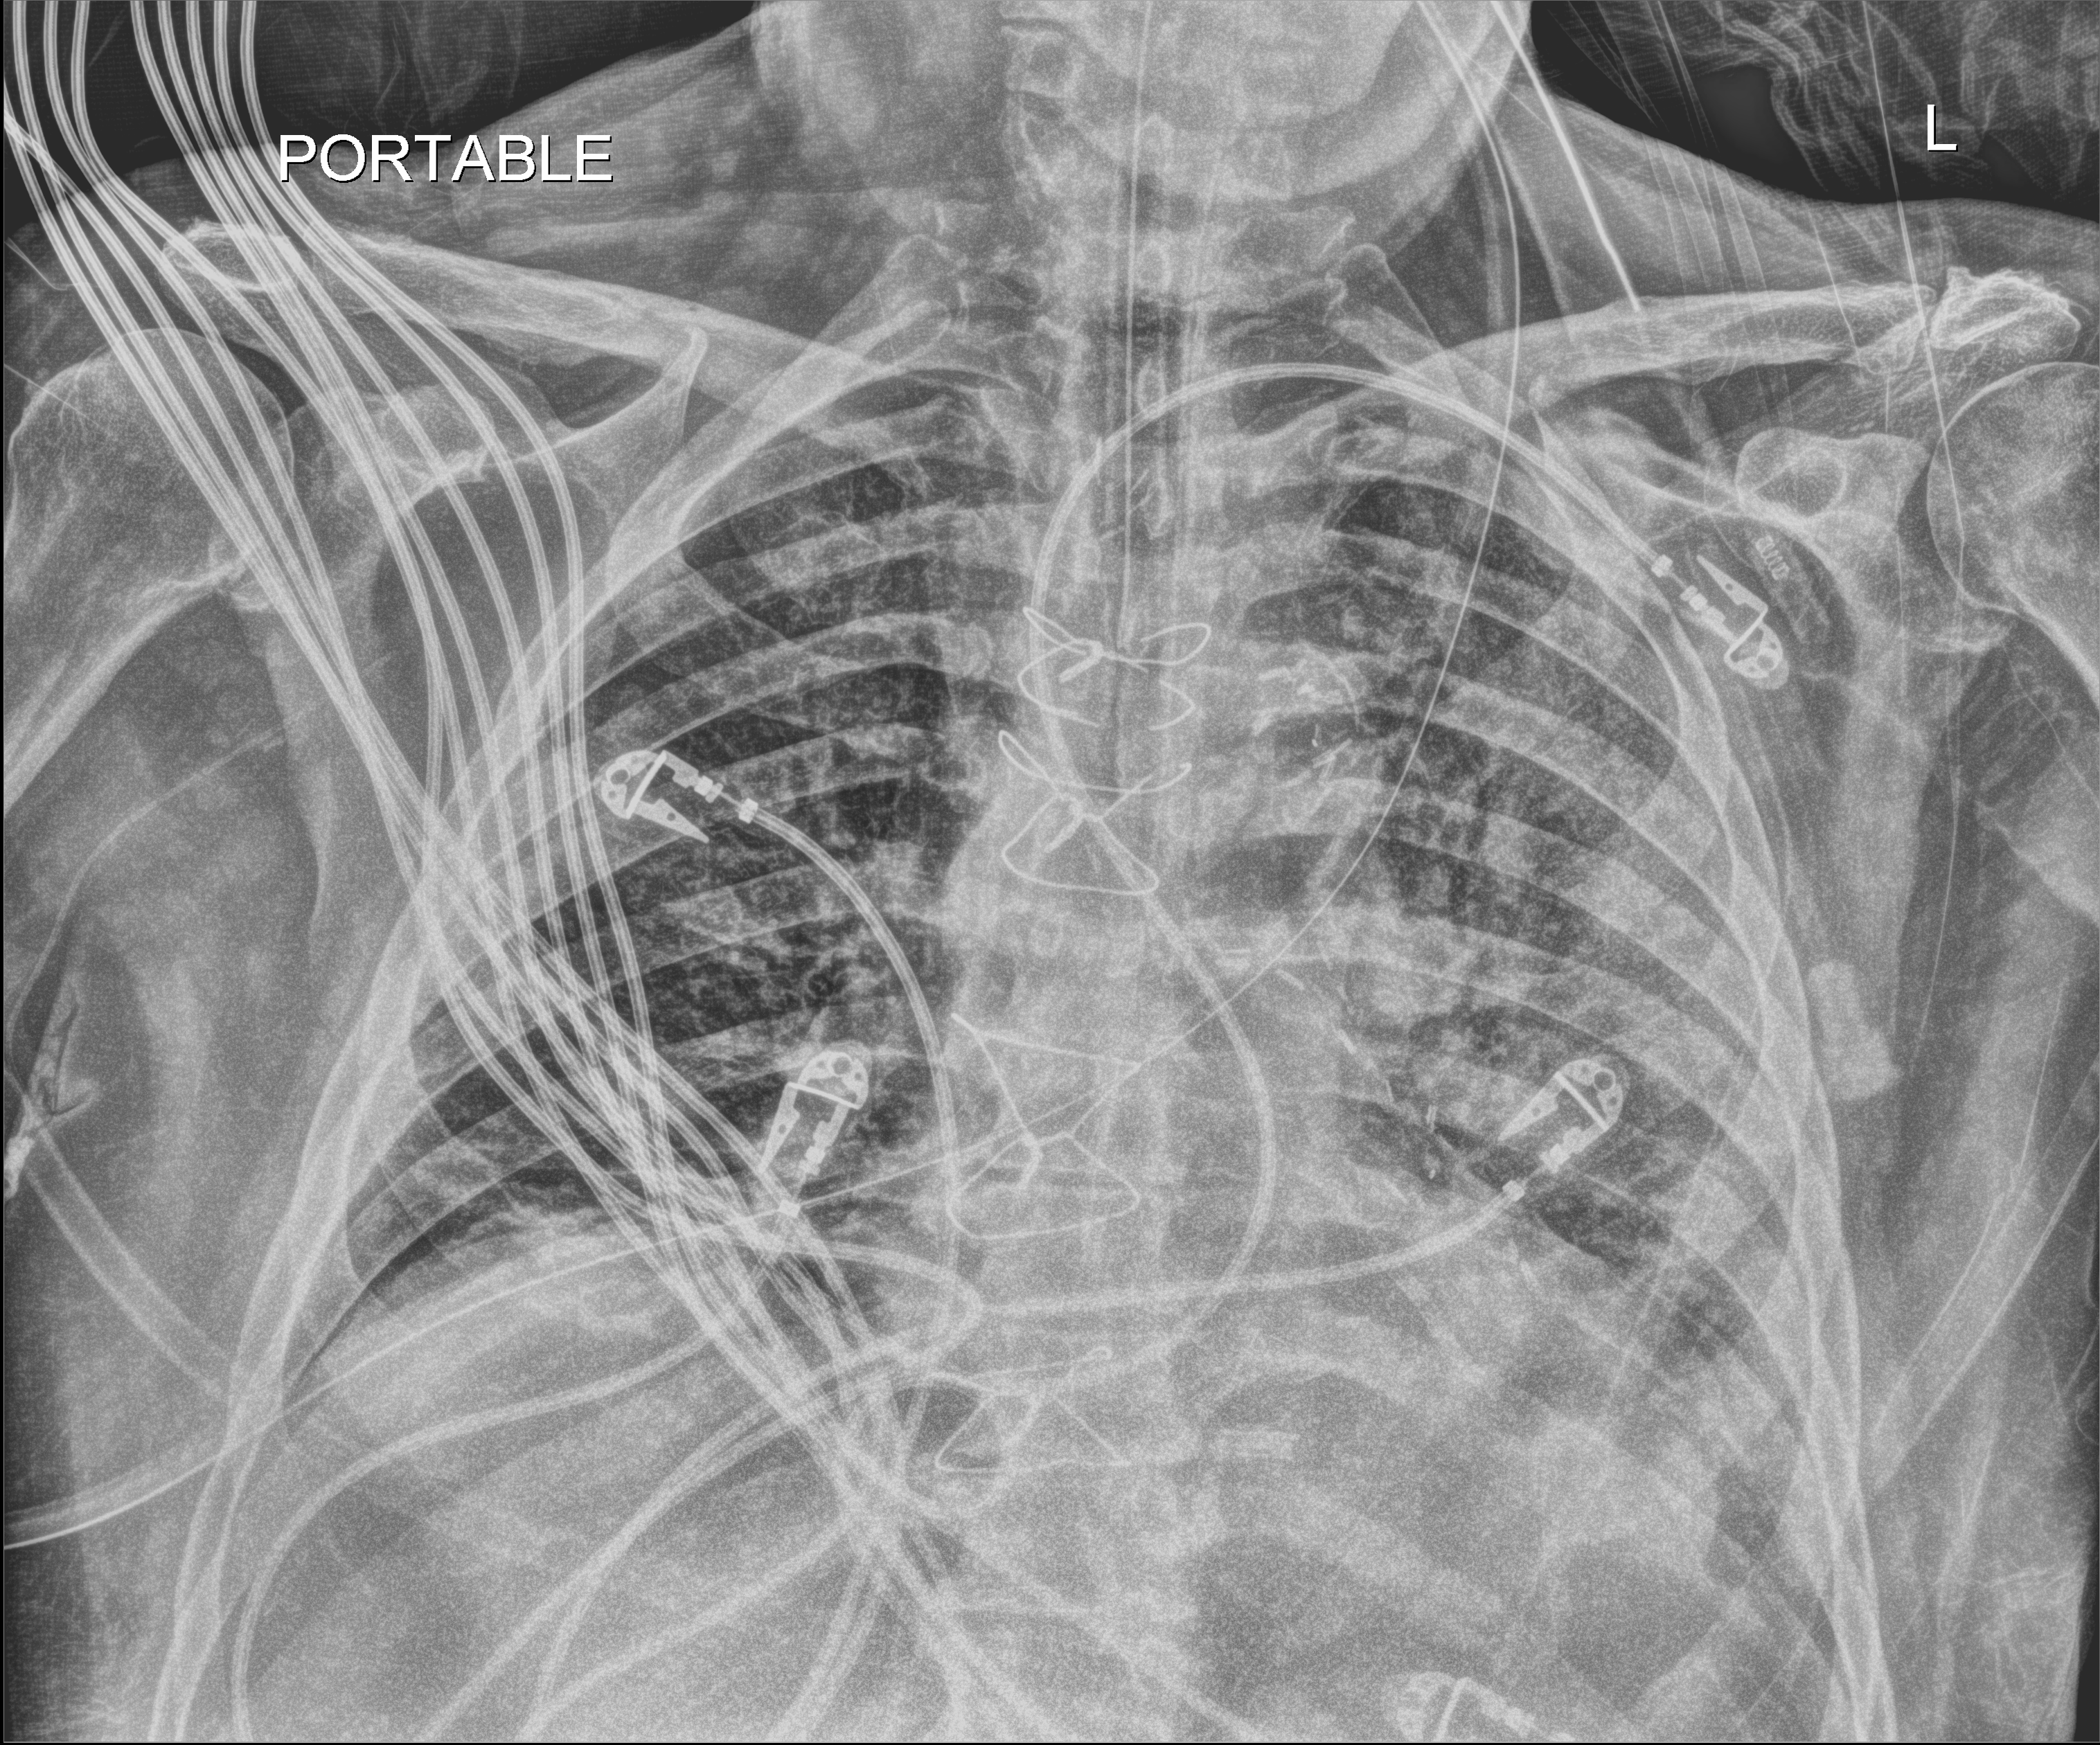
Chest X-ray (portable), anteroposterior (AP) projection. Patient hospitalised with COVID-19; male, aged 60–74 years.
Admission-level facts for this patient (not findings on this image; timing relative to this image not recorded): diabetes (admission record): yes.